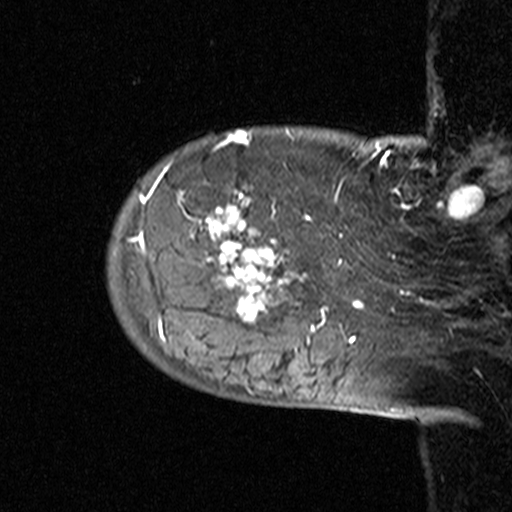
Breast MRI (dynamic contrast-enhanced), one sagittal slice; slice 7 of 44 in the series (ordered by position); dynamic contrast-enhanced study with each time point stored as its own series, time point 2 of 3 at this slice position (early post-contrast, ordered by acquisition time); 1.5 T; TE 4.5 ms, TR 11 ms; 3 mm slice thickness; 512 × 512 image matrix. Female patient, age 53 years. Case-level facts recorded for this patient, not image findings: setting: breast cancer imaged before/during neoadjuvant chemotherapy; receptor status: HR-positive, HER2-negative.
Outlined on this slice (semi-automatic segmentation, software-assisted and operator-edited):
- analysis volume of interest (the breast-tissue region the enhancement analysis was run in; not a lesion): bounding box [x1, y1, x2, y2] px = [106, 140, 311, 353]
- tumour enhancement mask (voxels above the 90 % enhancement threshold inside the analysis volume of interest): [139, 140, 308, 340]